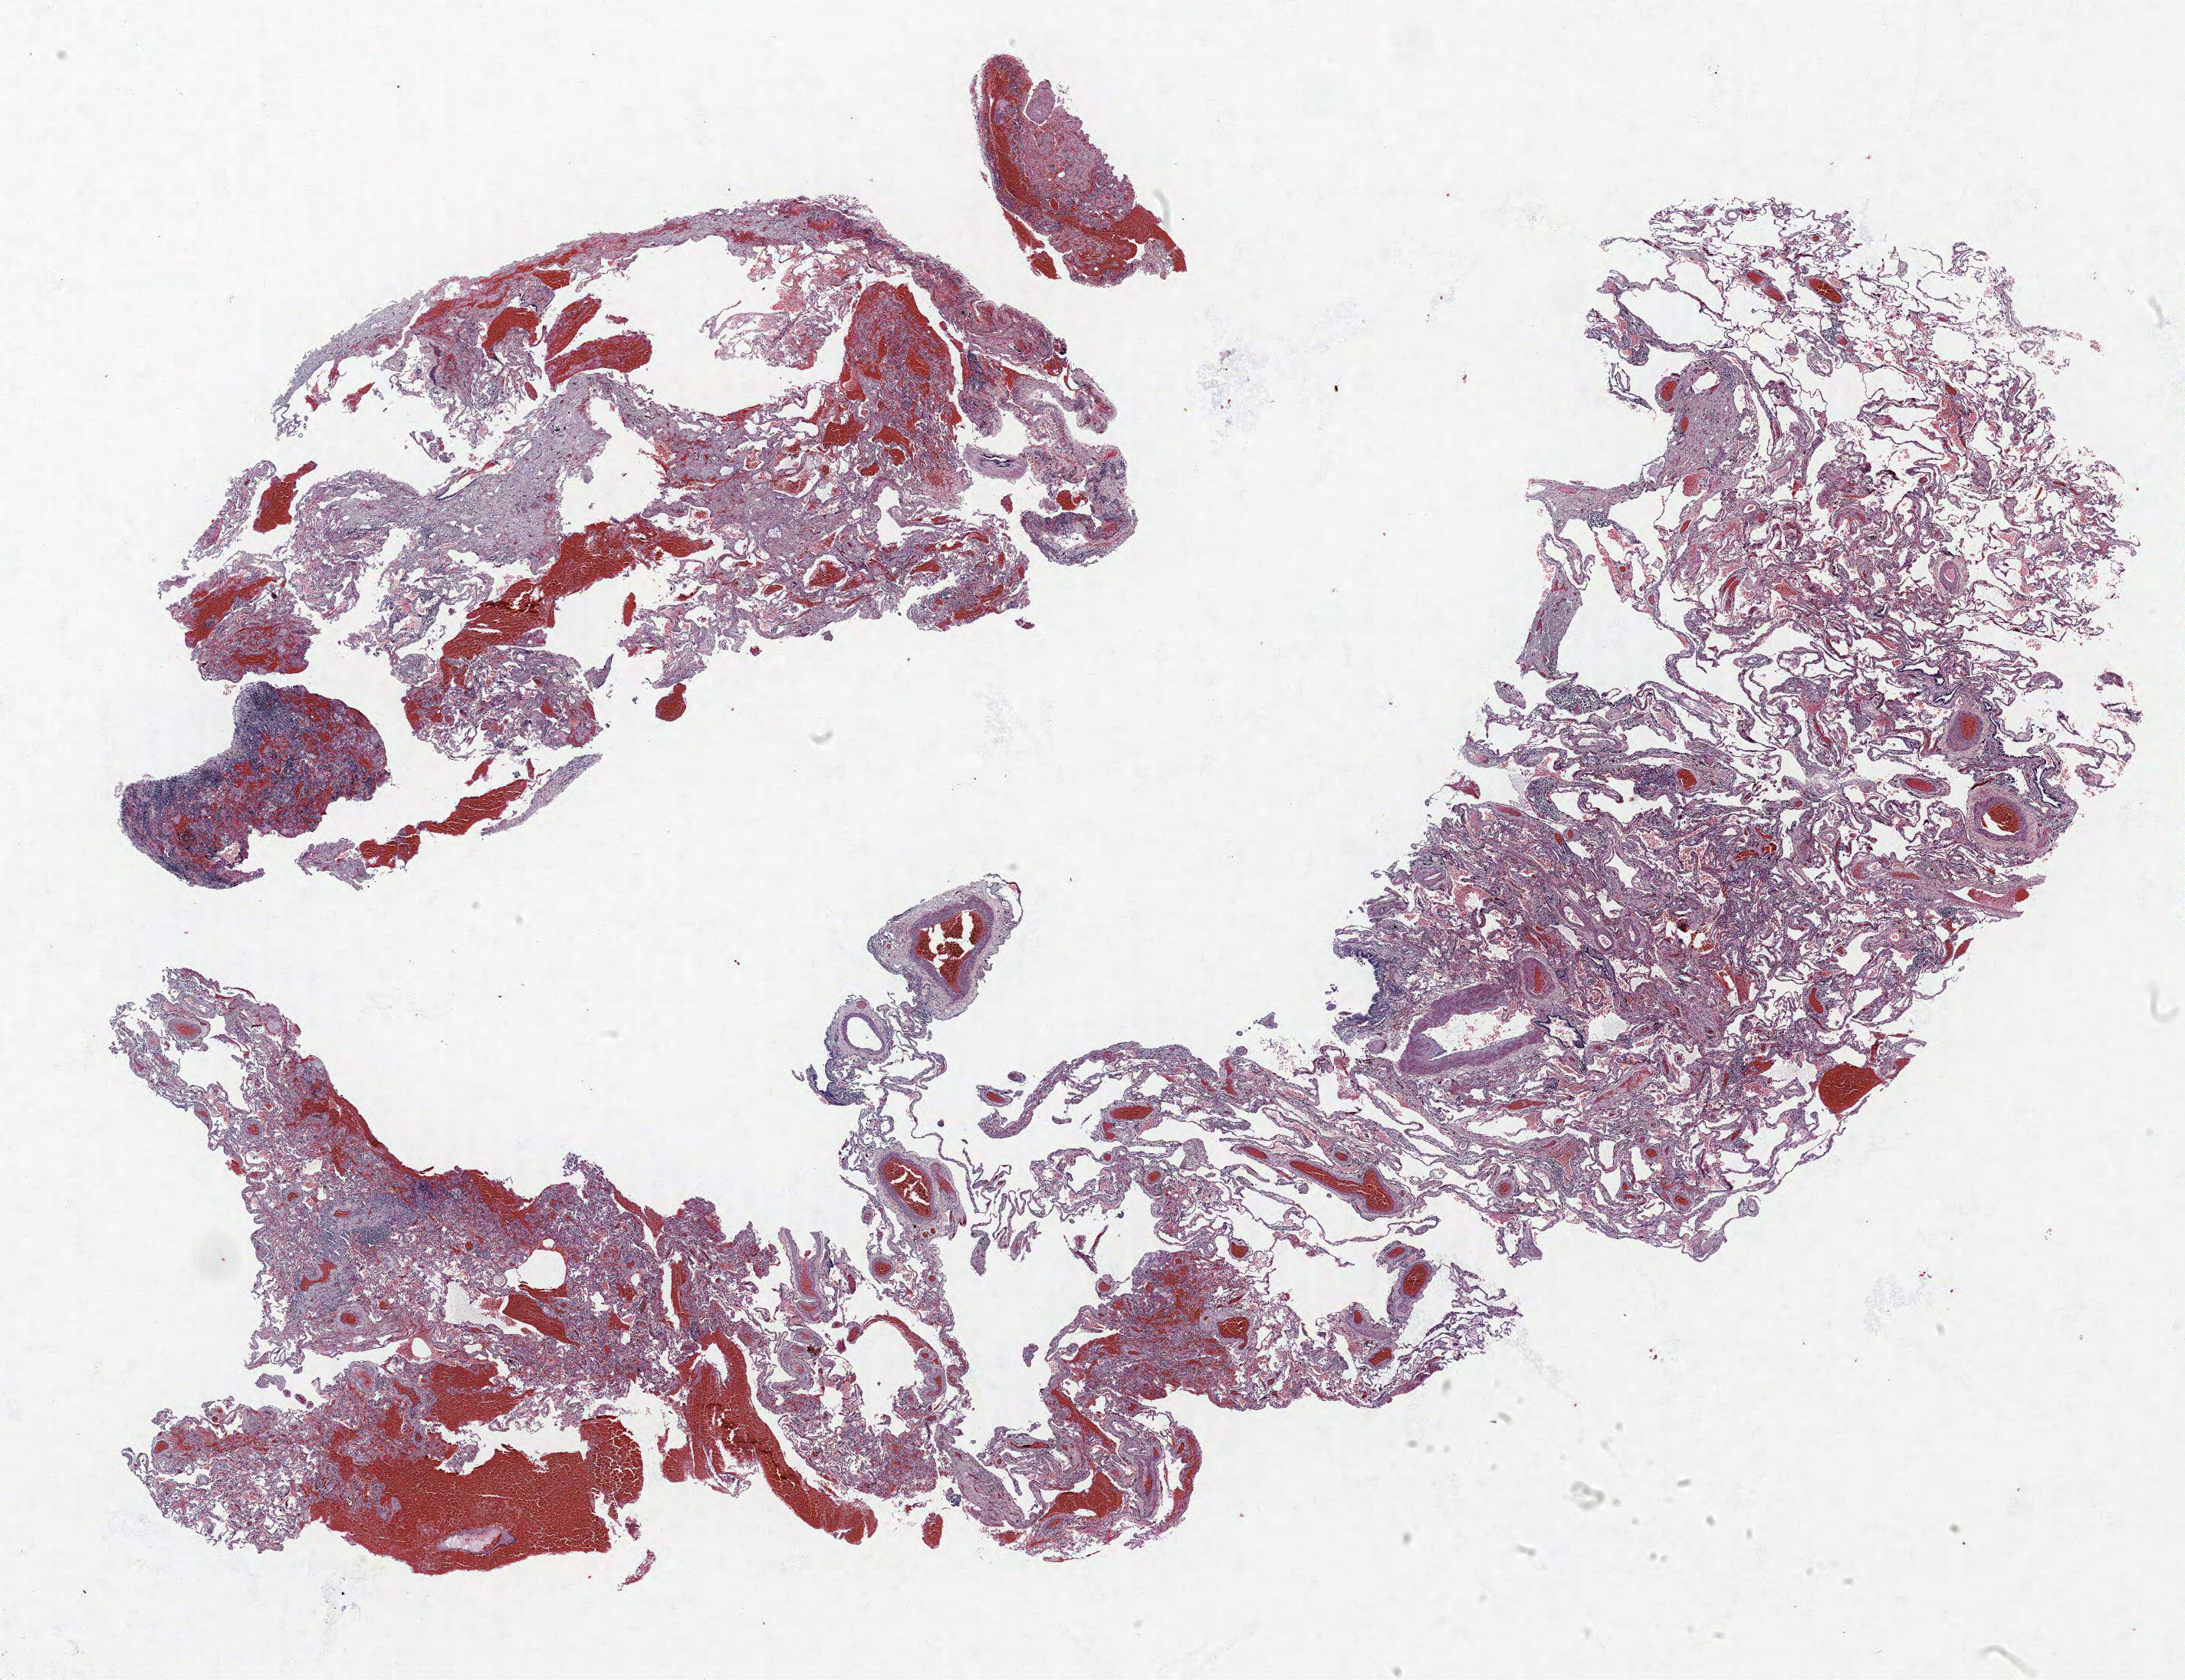
Hematoxylin and eosin (H&E) stained whole-slide image, whole scanned area (about 22.8 x 17.5 mm, acquisition: 40x scan) shown as a low-resolution overview; FFPE section; lung tissue. Male patient, aged 72 at enrolment. Former smoker at enrolment.
Participant's lung-cancer diagnosis: Squamous cell carcinoma, NOS.